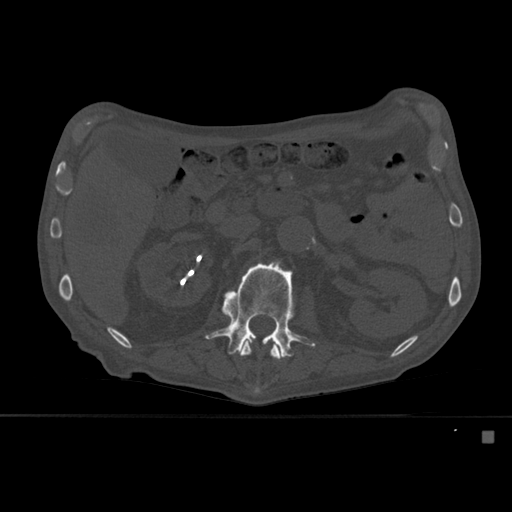
CT including the spine, one axial slice. Position 240 of 527 along the scan axis. Bone window (W 1800 / L 400 HU). 512 × 512 image matrix, field of view 373 × 373 mm. Patient: male, 78 years. From the clinical record (not read from this slice): primary cancer: prostate.
Structures marked on this image (semi-automatically segmented with operator editing):
- L1 vertebra: bounding box (x1, y1, x2, y2) in pixels: (240, 341, 282, 394)
- L2 vertebra: (205, 260, 316, 358)